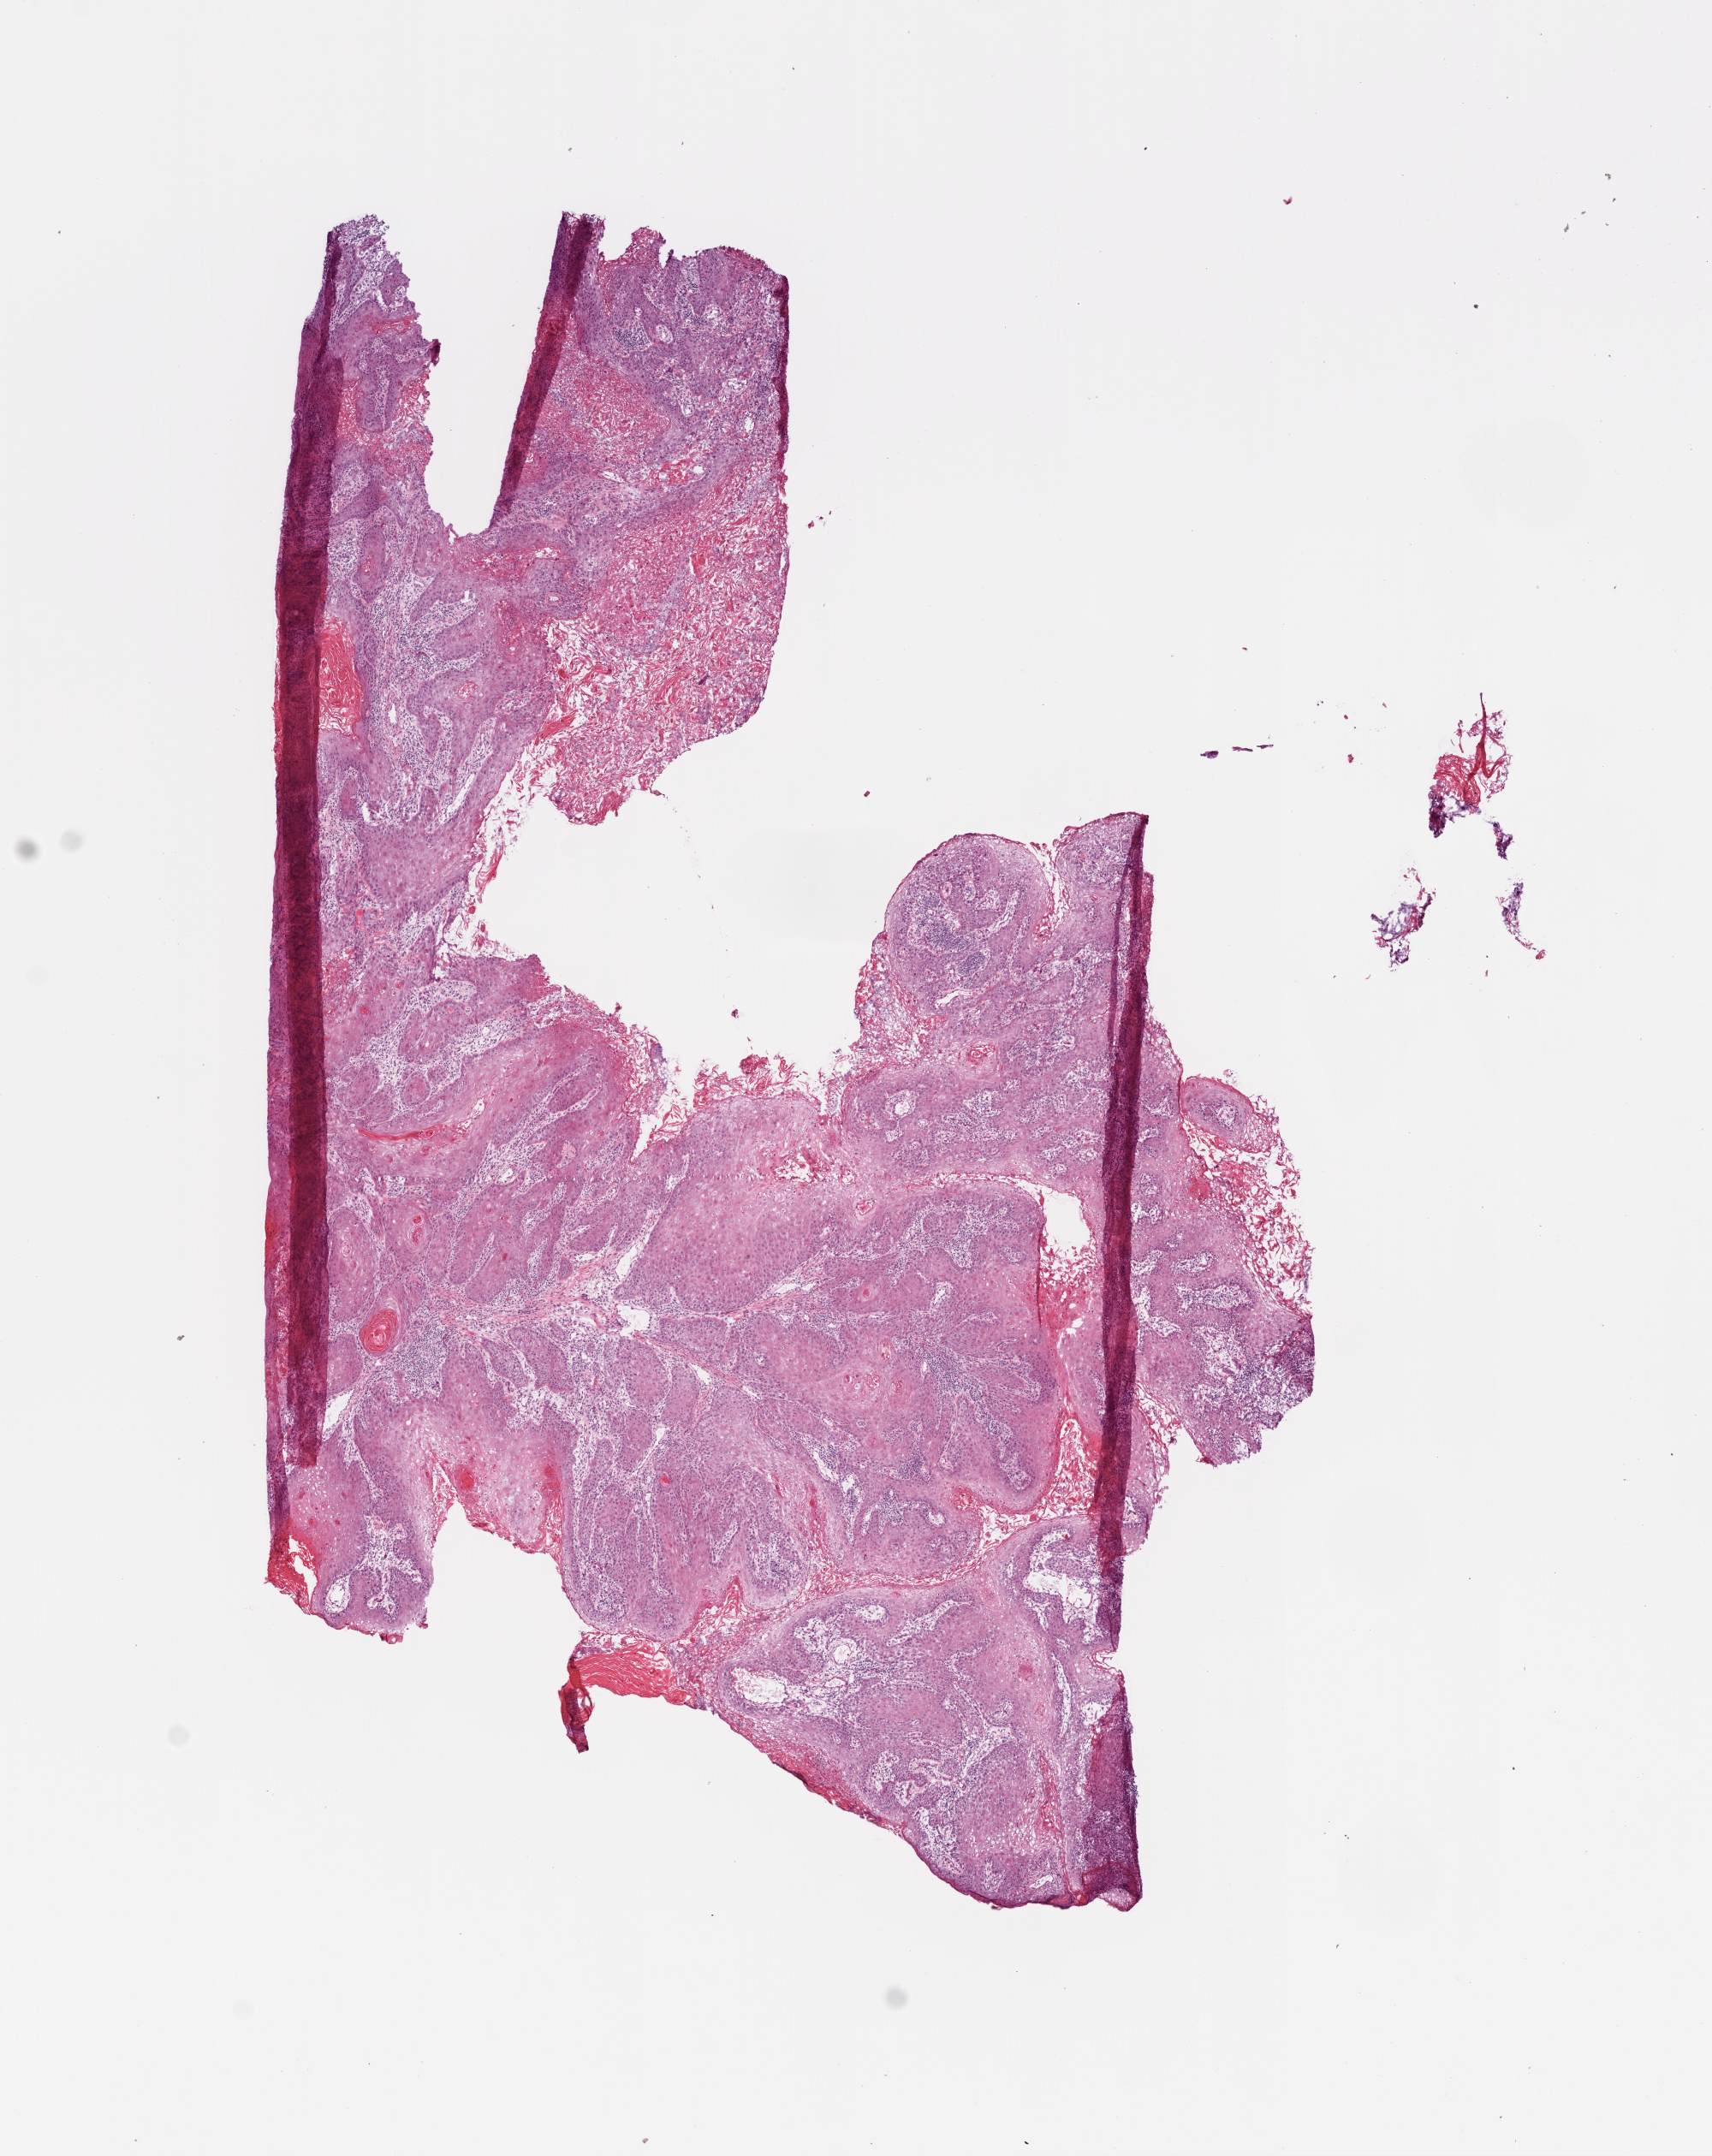
Whole-slide histology image, H&E-stained — low-resolution overview of the scanned area, about 8.0 x 10.1 mm (slide scanned at 20x), frozen section from the bottom of the tissue portion, sample: primary tumour, head and neck. Male, age 72 years at initial diagnosis. Histologic grade: G1 (well differentiated). Slide review estimates, as recorded: tumour cells 85%, tumour nuclei 70%, normal cells 0%, stromal cells 15%, necrosis 0%.
• histologic diagnosis: Squamous cell carcinoma, NOS (cheek mucosa)
• AJCC pathologic stage: IVA
• laterality: left